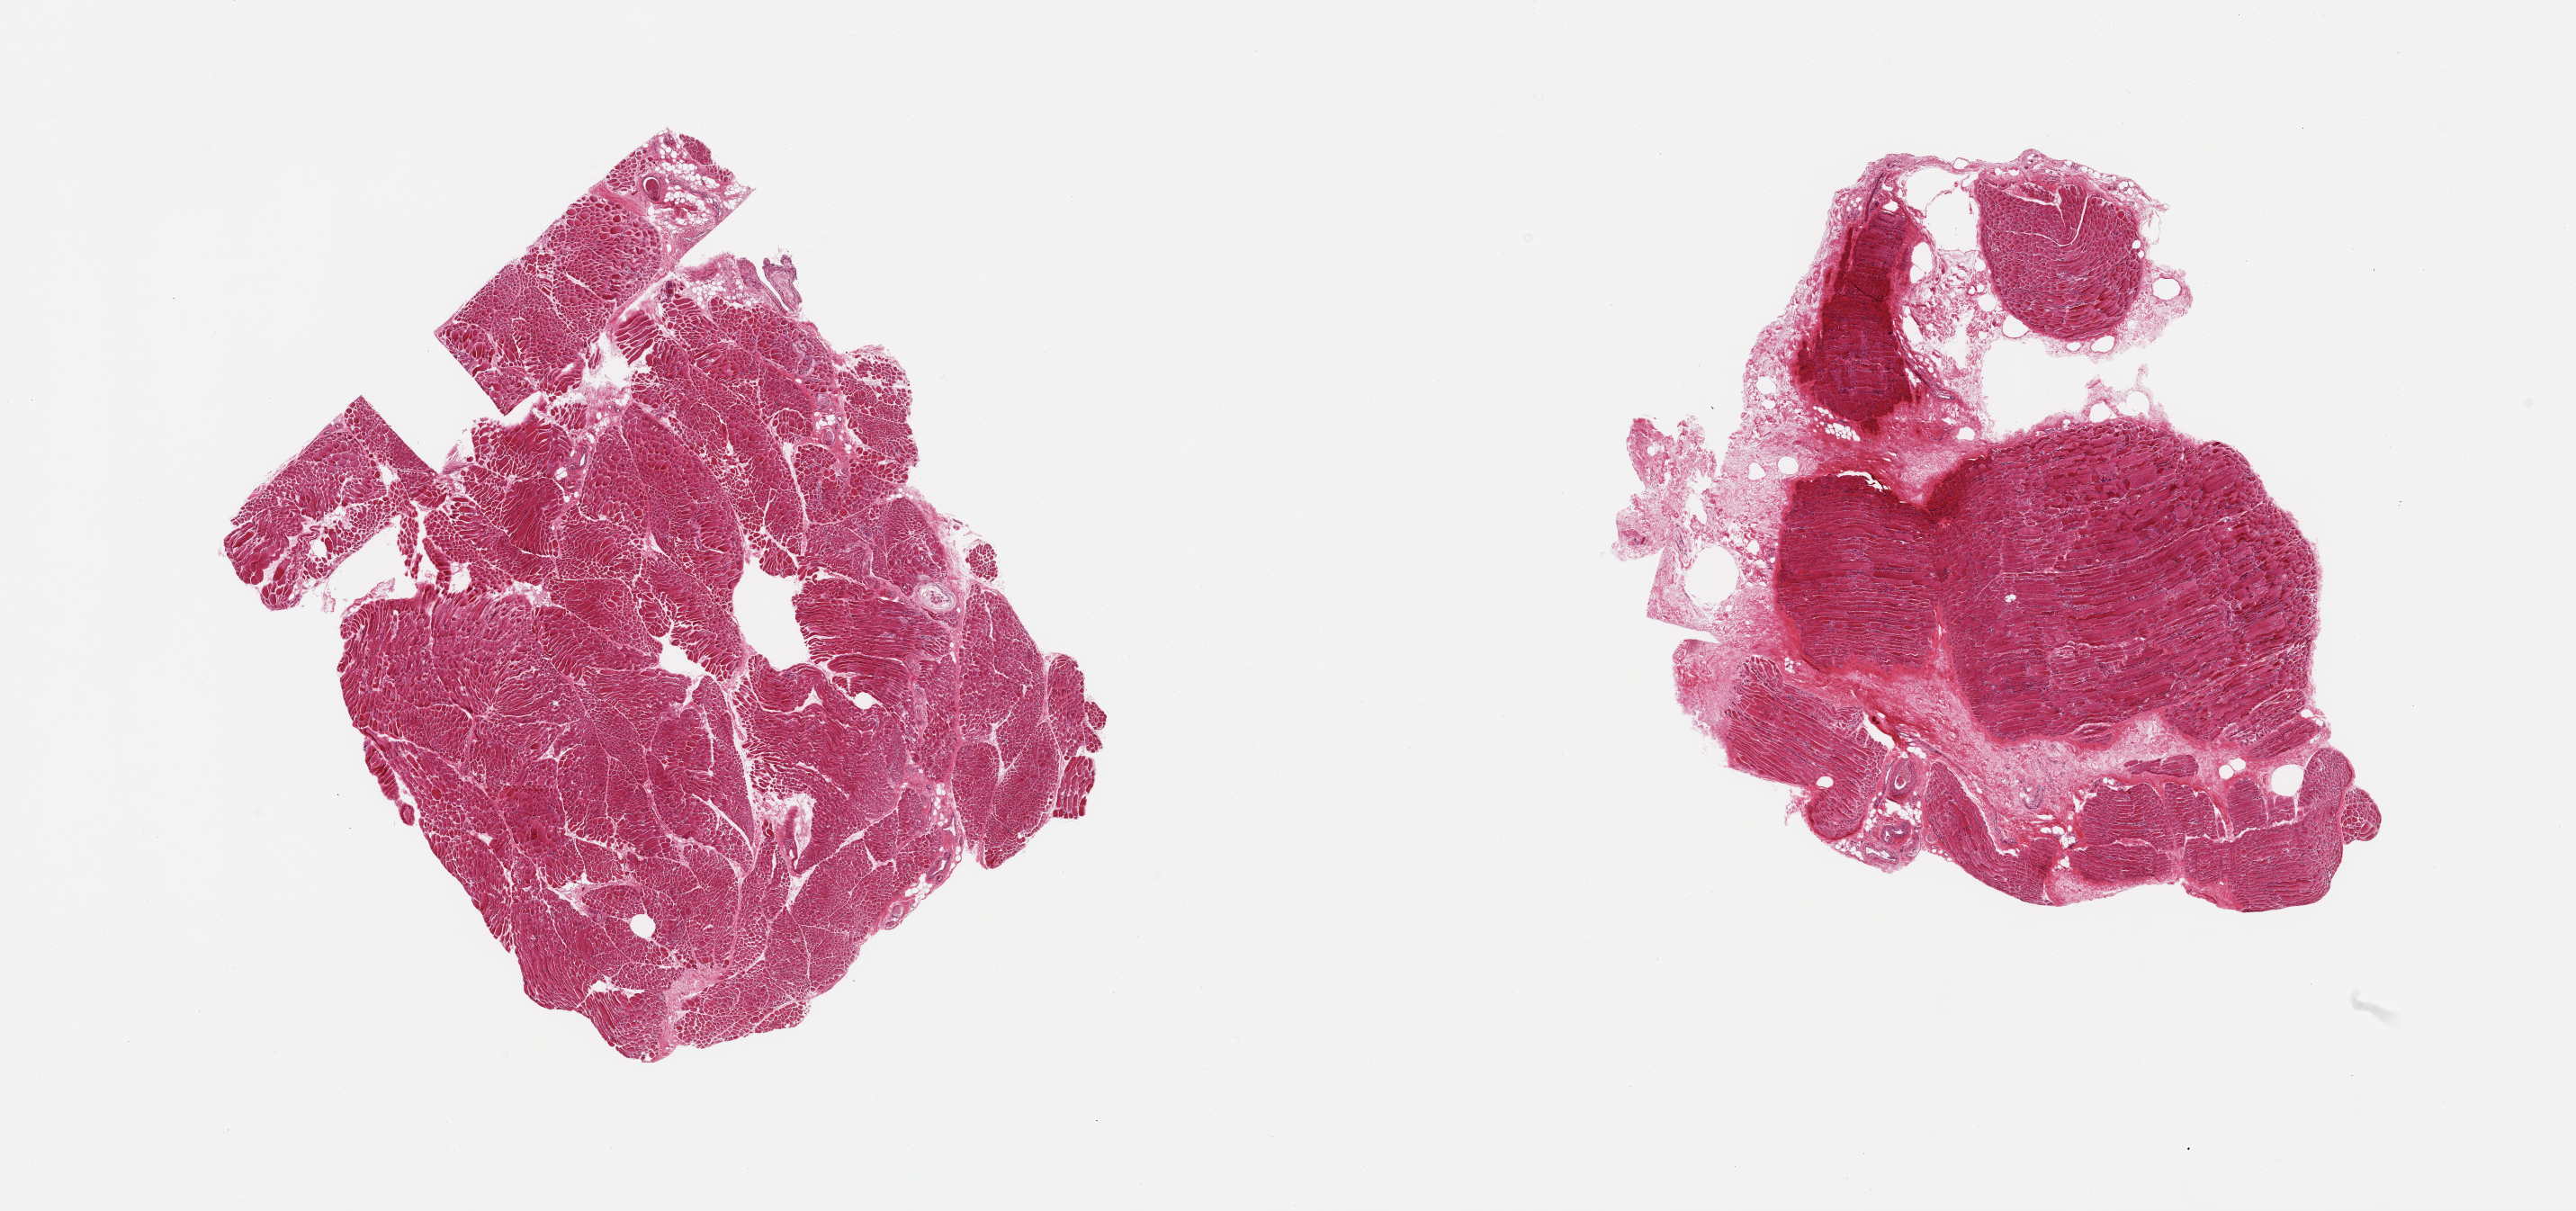
H&E whole-slide image, shown as a low-resolution overview of the whole scanned area (about 22.6 x 10.6 mm, from a 20x scan); PAXgene-fixed, paraffin-embedded tissue; sampled site (target tissue): skeletal muscle; donor tissue sample. Donor sex: male.
Reviewer comment on this tissue sample: 2 pieces; 1 piece shows vacuolization and atrophy with 25% internal fibrous content; other is largely normal.